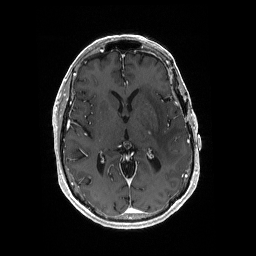
Brain MRI from a brain-tumour surgery series, one axial slice. Position 101 of 176 along the scan axis. T1-weighted post-contrast. 1 mm slice thickness. 256 × 256 image matrix, field of view 256 × 256 mm. Case-level facts recorded for this patient, not image findings: histopathology: Glioblastoma; WHO grade: 4; IDH mutation: no; tumour location: Left Medial Temporal.
Annotated regions visible in this slice (manually delineated by an expert):
- tumour: box from (x=147, y=131) to (x=151, y=135) px